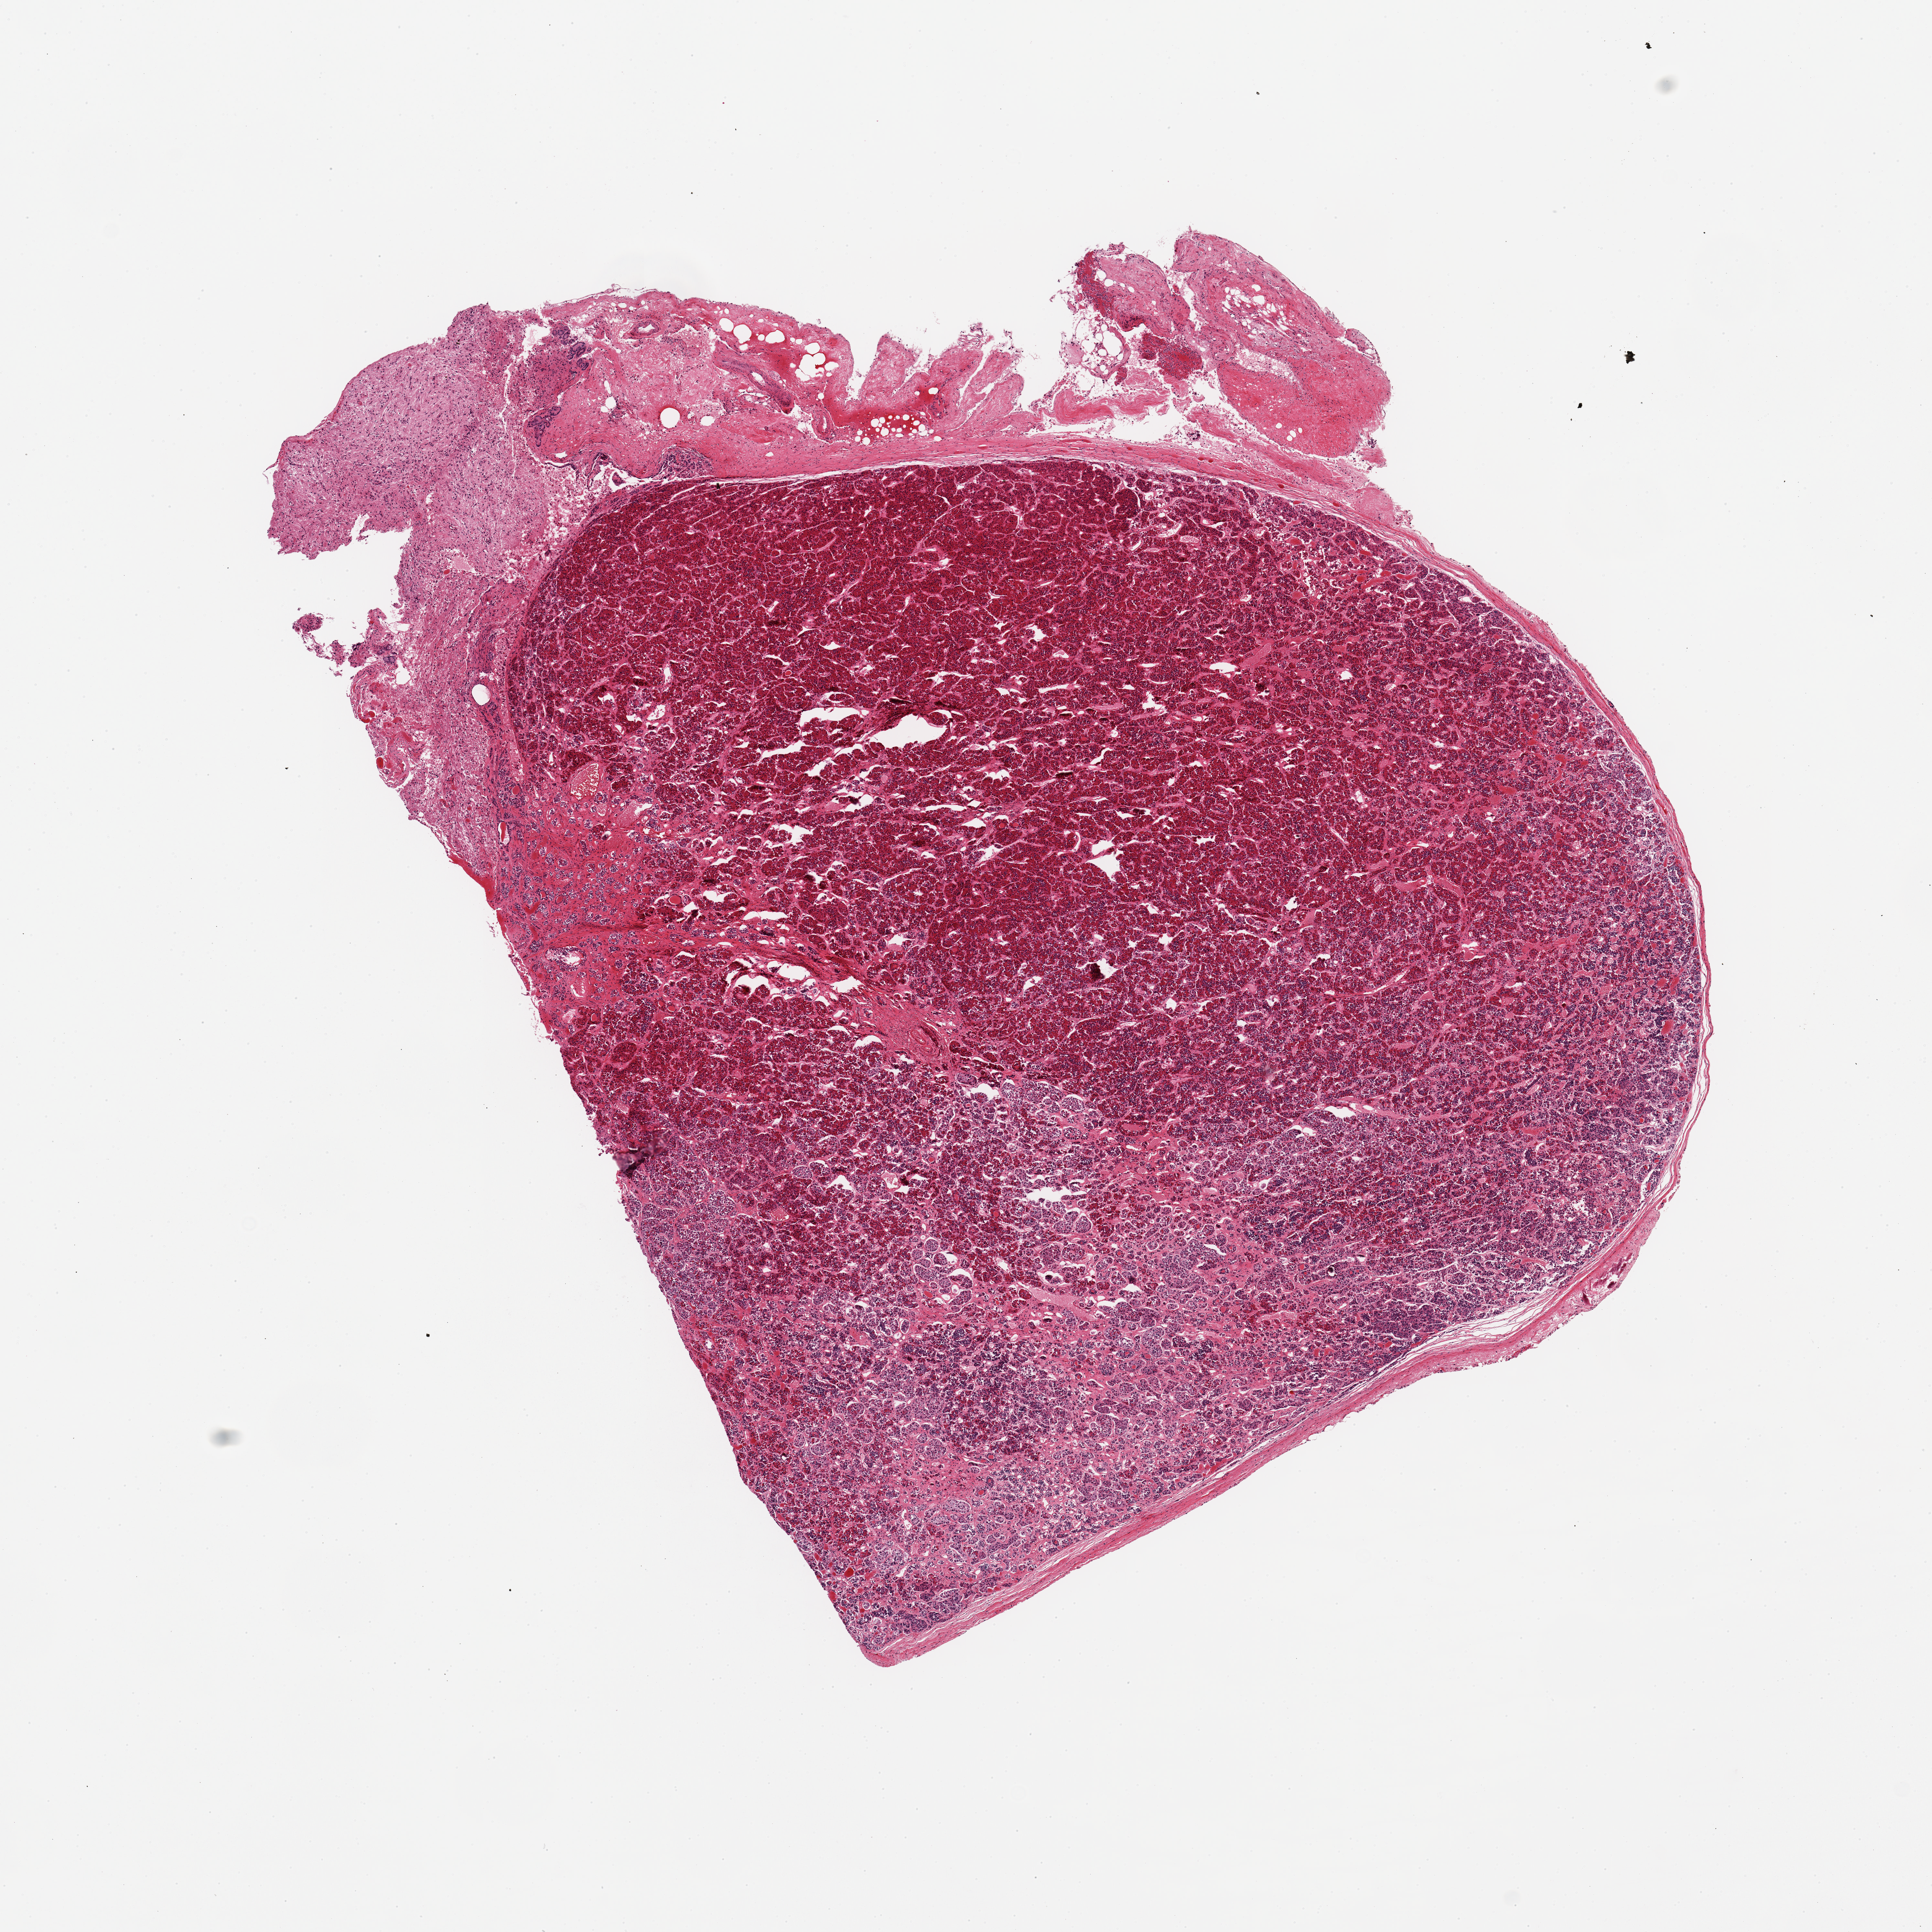
Whole-slide image, haematoxylin and eosin stain — whole scanned area (about 11.8 x 11.8 mm, acquisition: 20x scan) shown as a low-resolution overview, PAXgene-fixed paraffin-embedded (PFPE) section, section of pituitary (target tissue), donor tissue sample. Donor sex: female.
- review note (as recorded): 1 piece; 80% anterior hypophysis; posterior